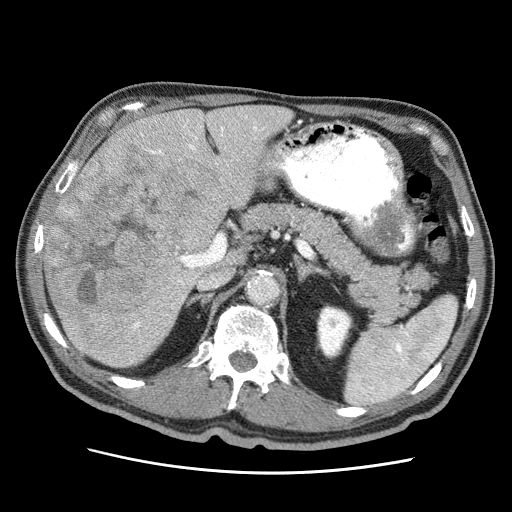
Contrast-enhanced abdominal CT (liver protocol), one axial slice. Slice 27 of 75 in the series (ordered by position). Reconstruction kernel STANDARD. 120 kVp. Soft-tissue window (W 400 / L 40 HU). 512 × 512 image matrix. Case-level facts recorded for this patient, not image findings: diagnosis: hepatocellular carcinoma (patient treated with transarterial chemoembolisation; whether this scan precedes or follows treatment is not stated here); TNM stage (as recorded): Stage-IIIA; Child-Pugh class: A; tumour differentiation: well differentiated; tumour nodularity: multinodular.
Annotated regions visible in this slice (semi-automatic segmentation, software-assisted and operator-edited):
- liver parenchyma outside the tumour (the mass and vessels are separate outlines, so this box may not span the whole liver): bounding box [x1, y1, x2, y2] px = [44, 104, 292, 367]
- mass: [48, 137, 221, 355]
- liver vessels: [132, 115, 265, 330]